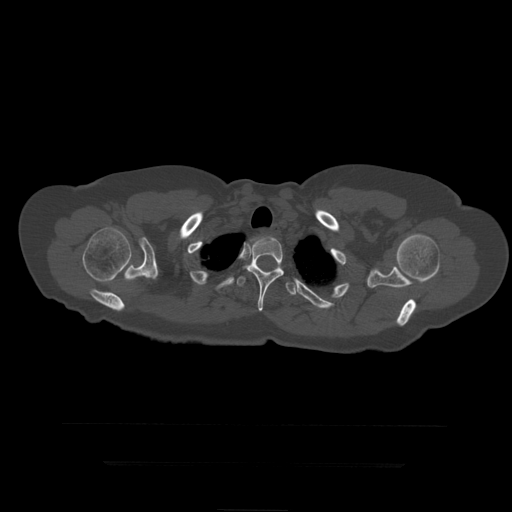
CT including the spine, one axial slice. Position 362 of 399 along the scan axis. 120 kVp. Bone window (W 1800 / L 400 HU). 512 × 512 image matrix. Patient age 41 years. Case-level facts recorded for this patient, not image findings: primary cancer: breast.
Structures marked on this image (semi-automatically segmented with operator editing):
- T2 vertebra: bounding box [x1, y1, x2, y2] px = [250, 239, 256, 243]
- T3 vertebra: [243, 236, 284, 312]
- T4 vertebra: [237, 266, 298, 295]